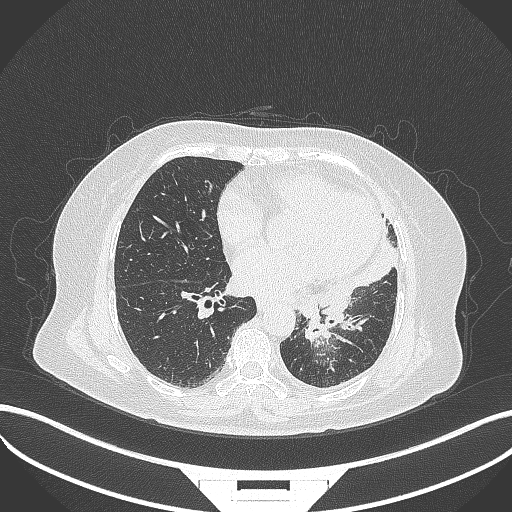
Chest CT, one axial slice. Position 146 of 322 along the scan axis. Reconstruction kernel B70f. Lung window (W 1500 / L -600 HU). 1 mm slice thickness. 512 × 512 image matrix, field of view 400 × 400 mm. Female patient, age 69 years. Case-level facts recorded for this patient, not image findings: clinical TNM (as recorded): T2b N3 M1.
Annotated regions visible in this slice (rectangle marked by the reading radiologist):
- lung tumour (recorded histology: adenocarcinoma): bounding box (x1, y1, x2, y2) in pixels: (295, 304, 332, 346)